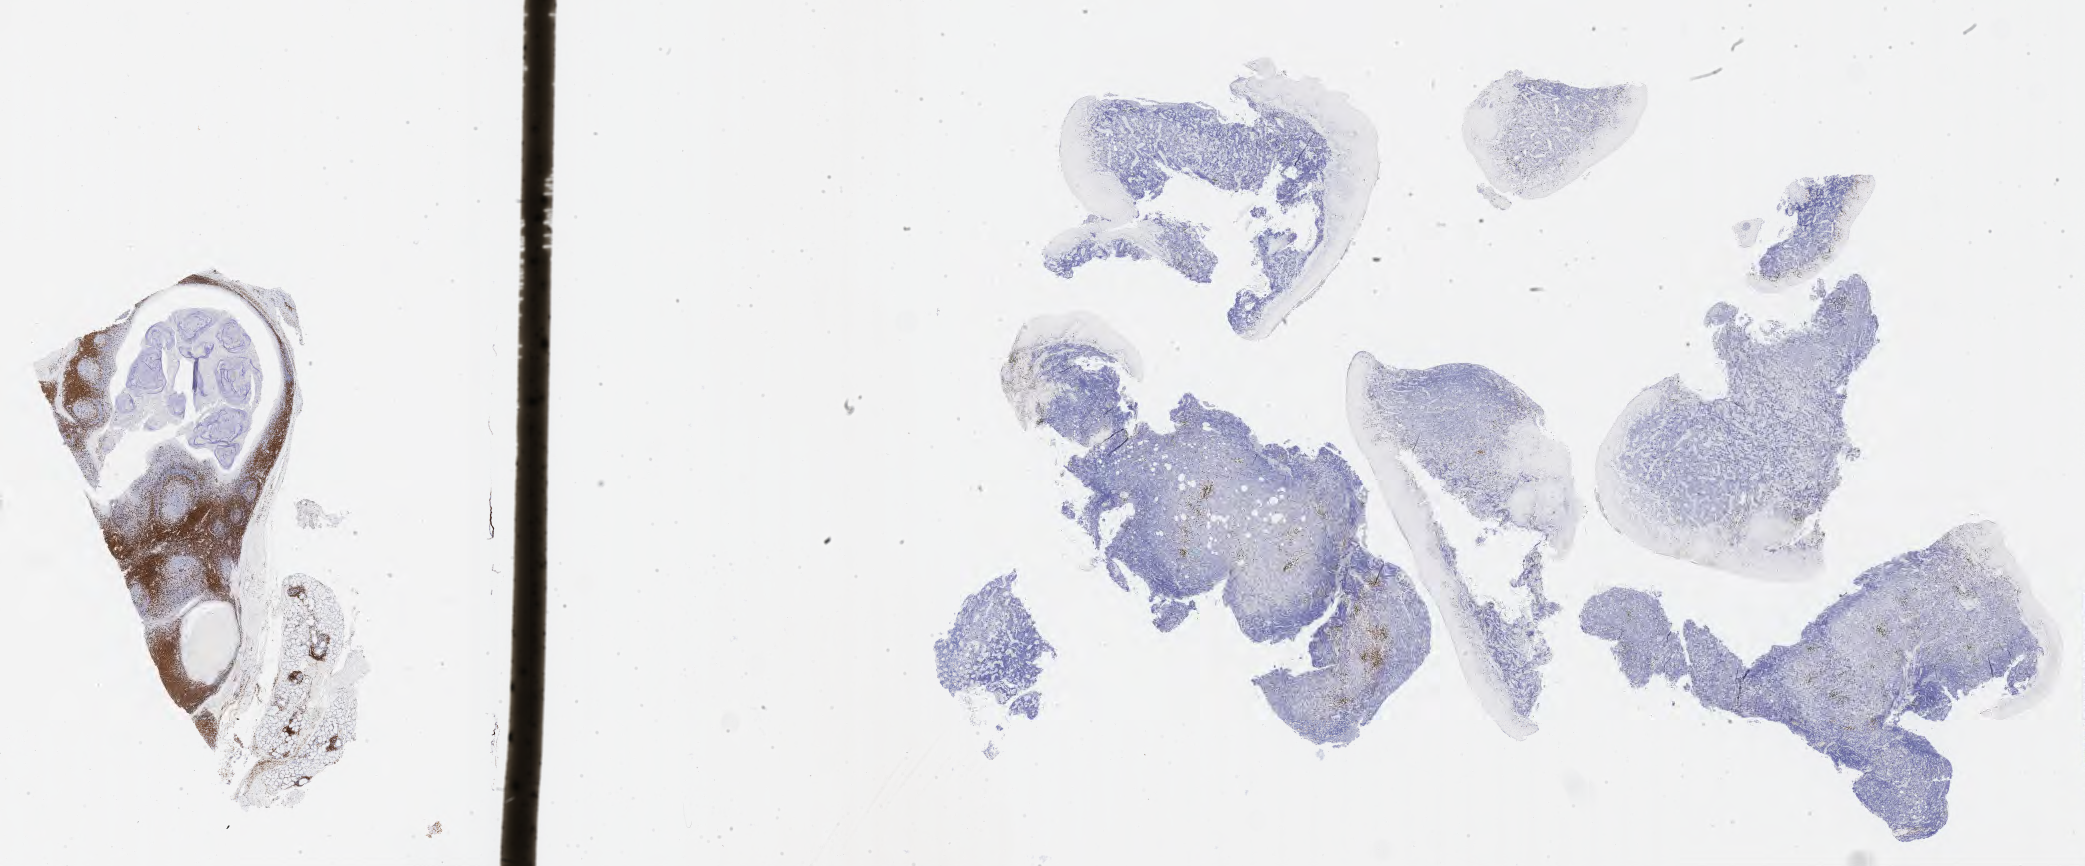
Immunohistochemistry (IHC) whole-slide image stained for CD3 — shown as a low-resolution overview of the whole scanned area (about 33.7 x 14.0 mm), tumor tissue. Male patient, aged 43.
Diagnosis: Burkitt lymphoma, NOS.